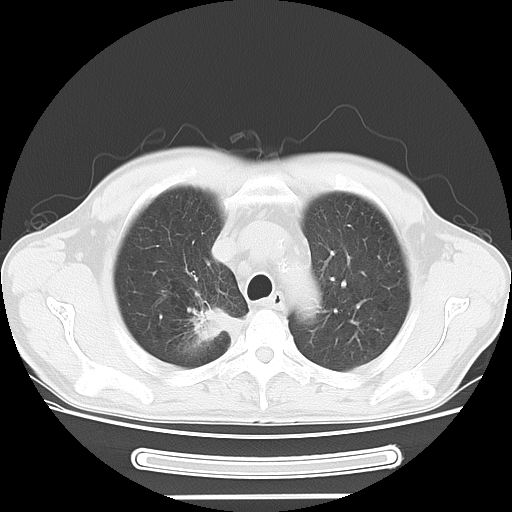
Chest CT, one axial slice. Position 39 of 51 along the scan axis. Reconstruction kernel LUNG. 120 kVp. Lung window (W 1500 / L -600 HU). 5 mm slice thickness. 512 × 512 image matrix. Male patient, age 57 years. From the clinical record (not read from this slice): clinical TNM (as recorded): T2 N3 M1b.
Annotated regions visible in this slice (rectangle marked by the reading radiologist):
- lung tumour (recorded histology: adenocarcinoma): bounding box (x1, y1, x2, y2) in pixels: (185, 299, 228, 341)